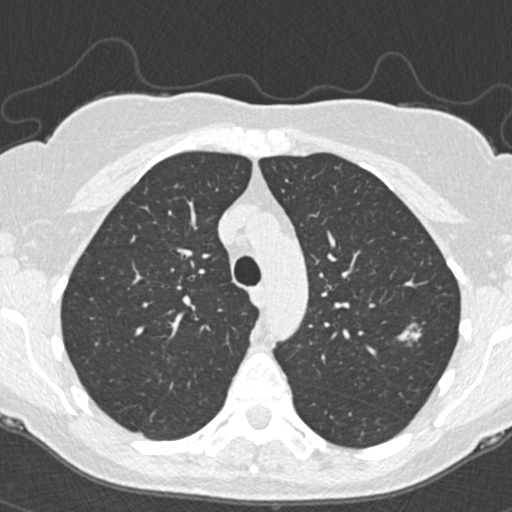
Low-dose screening chest CT, one axial slice; position 265 of 350 along the scan axis; reconstruction kernel B30f; 120 kVp; lung window (W 1500 / L -600 HU); 1 mm slice thickness; 512 × 512 image matrix, field of view 298 × 298 mm.
Structures marked on this image (expert manual segmentation):
- lesion 1 (tumor, upper lobe of left lung): bounding box (x1, y1, x2, y2) in pixels: (397, 323, 422, 341)